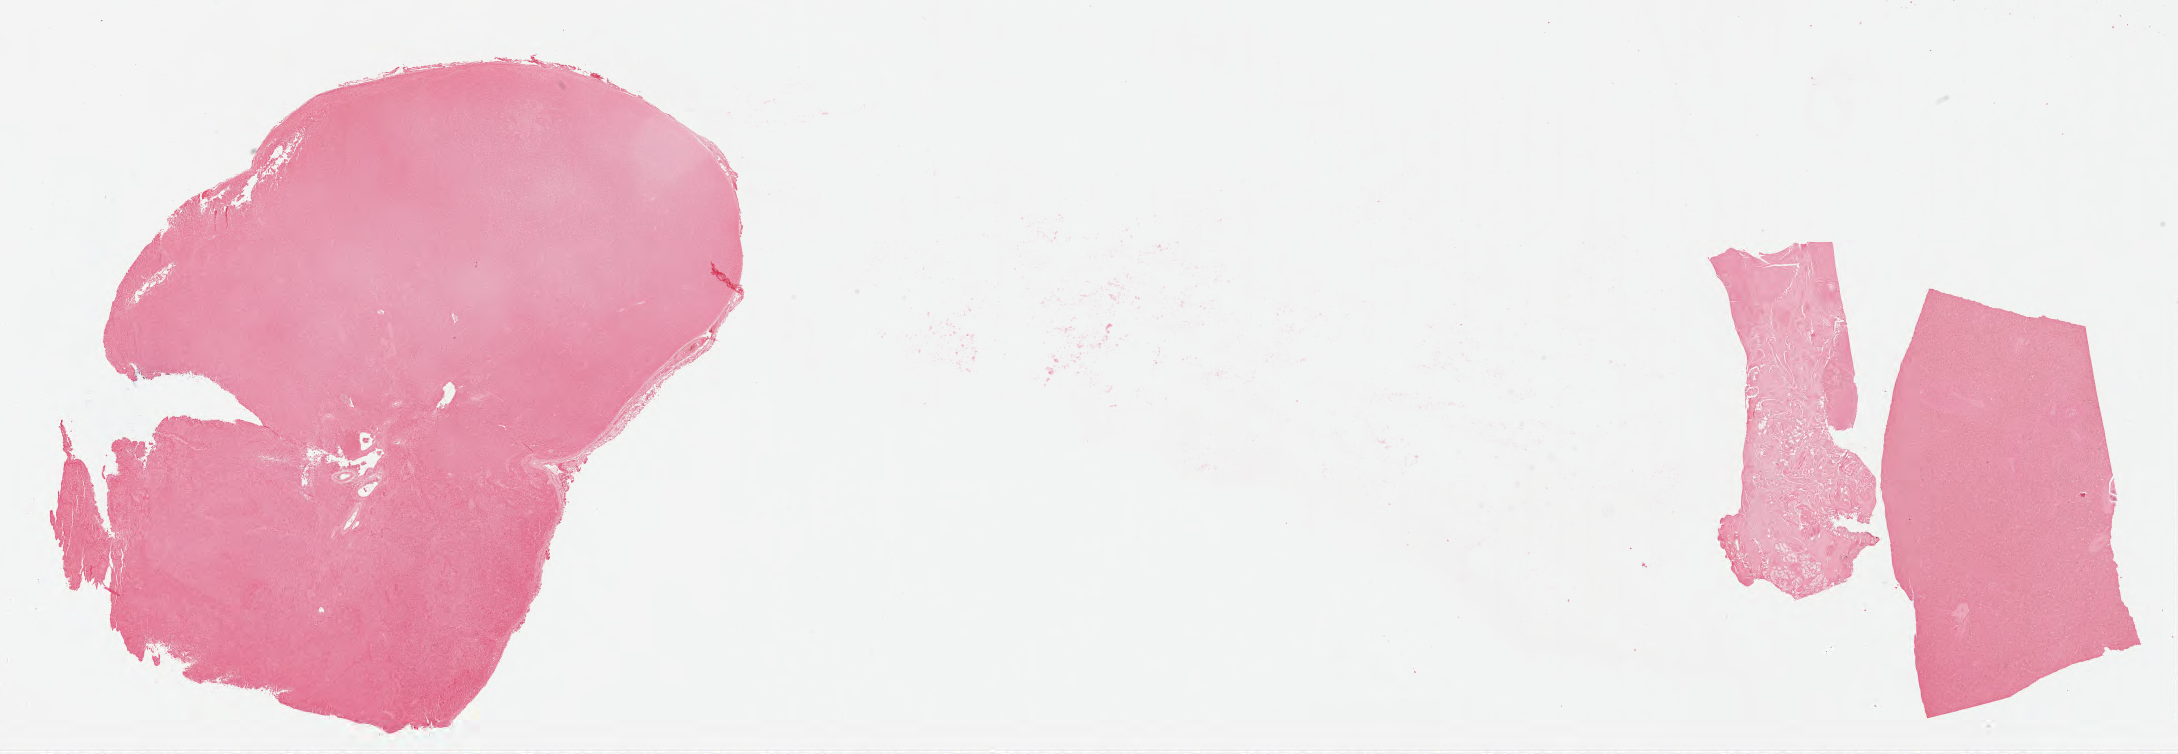
Whole-slide image, Epstein–Barr virus-encoded RNA (EBER) in-situ hybridisation — low-resolution overview of the scanned area, about 35.2 x 12.2 mm; tumor tissue; site: lymph node. Patient: male, aged 32.
Histologic diagnosis: Diffuse large B-cell lymphoma, NOS.